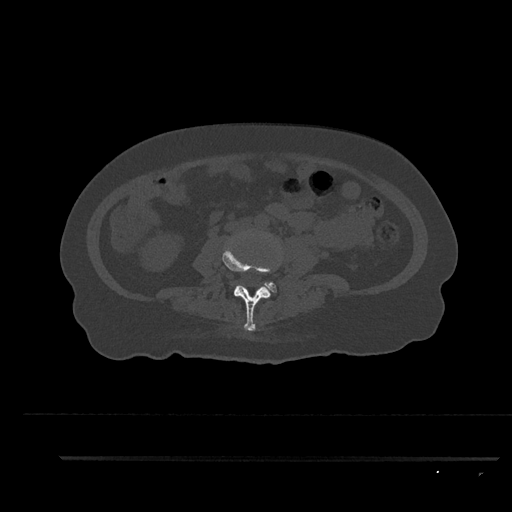
CT including the spine, one axial slice. Position 65 of 797 along the scan axis. Reconstruction kernel Br40s/3. 120 kVp. Bone window (W 1800 / L 400 HU). 0.5 mm slice thickness. 512 × 512 image matrix, field of view 408 × 408 mm. Patient: female, 44 years. From the clinical record (not read from this slice): primary cancer: renal; vertebrae with lytic lesions (as recorded): L1.
Structures marked on this image (semi-automatically segmented with operator editing):
- L3 vertebra: bounding box (x1, y1, x2, y2) in pixels: (222, 242, 281, 331)
- L4 vertebra: (262, 282, 277, 293)